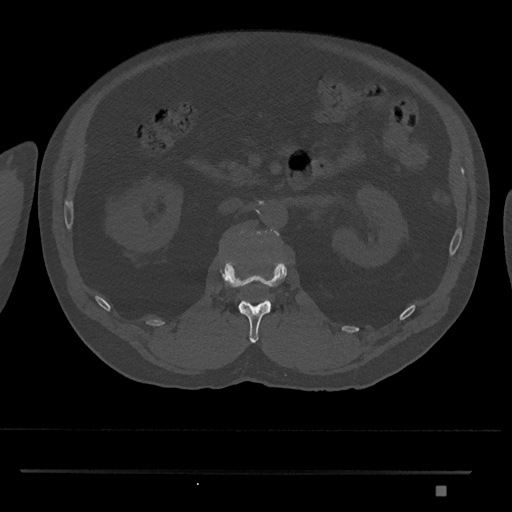
CT including the spine, one axial slice; position 800 of 1134 along the scan axis; 120 kVp; bone window (W 1800 / L 400 HU); 0.5 mm slice thickness; 512 × 512 image matrix, field of view 429 × 429 mm. Patient: male, 65 years. Case-level facts recorded for this patient, not image findings: primary cancer: prostate.
Annotated regions visible in this slice (semi-automatically segmented with operator editing):
- L1 vertebra: box from (x=220, y=261) to (x=287, y=343) px
- L2 vertebra: (x=238, y=229)–(x=280, y=243)